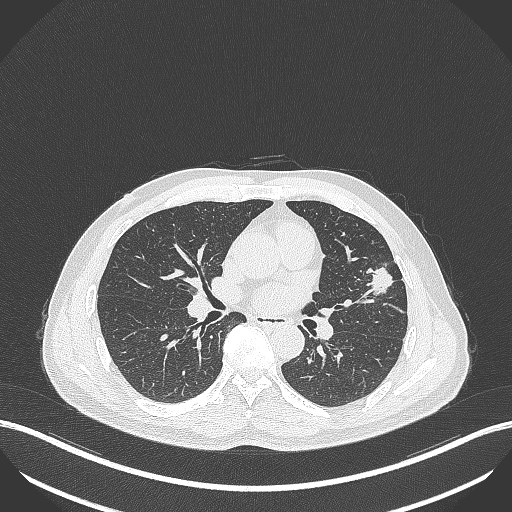
Chest CT, one axial slice. Reconstruction kernel B70f. 120 kVp. Lung window (W 1500 / L -600 HU). 1 mm slice thickness. 512 × 512 image matrix. Patient: male, 55 years. From the clinical record (not read from this slice): clinical TNM (as recorded): T1c N0 M0; histopathological grade: G2-3.
Outlined on this slice (bounding box drawn by a radiologist):
- lung tumour (recorded histology: adenocarcinoma): bounding box (x1, y1, x2, y2) in pixels: (367, 264, 395, 299)